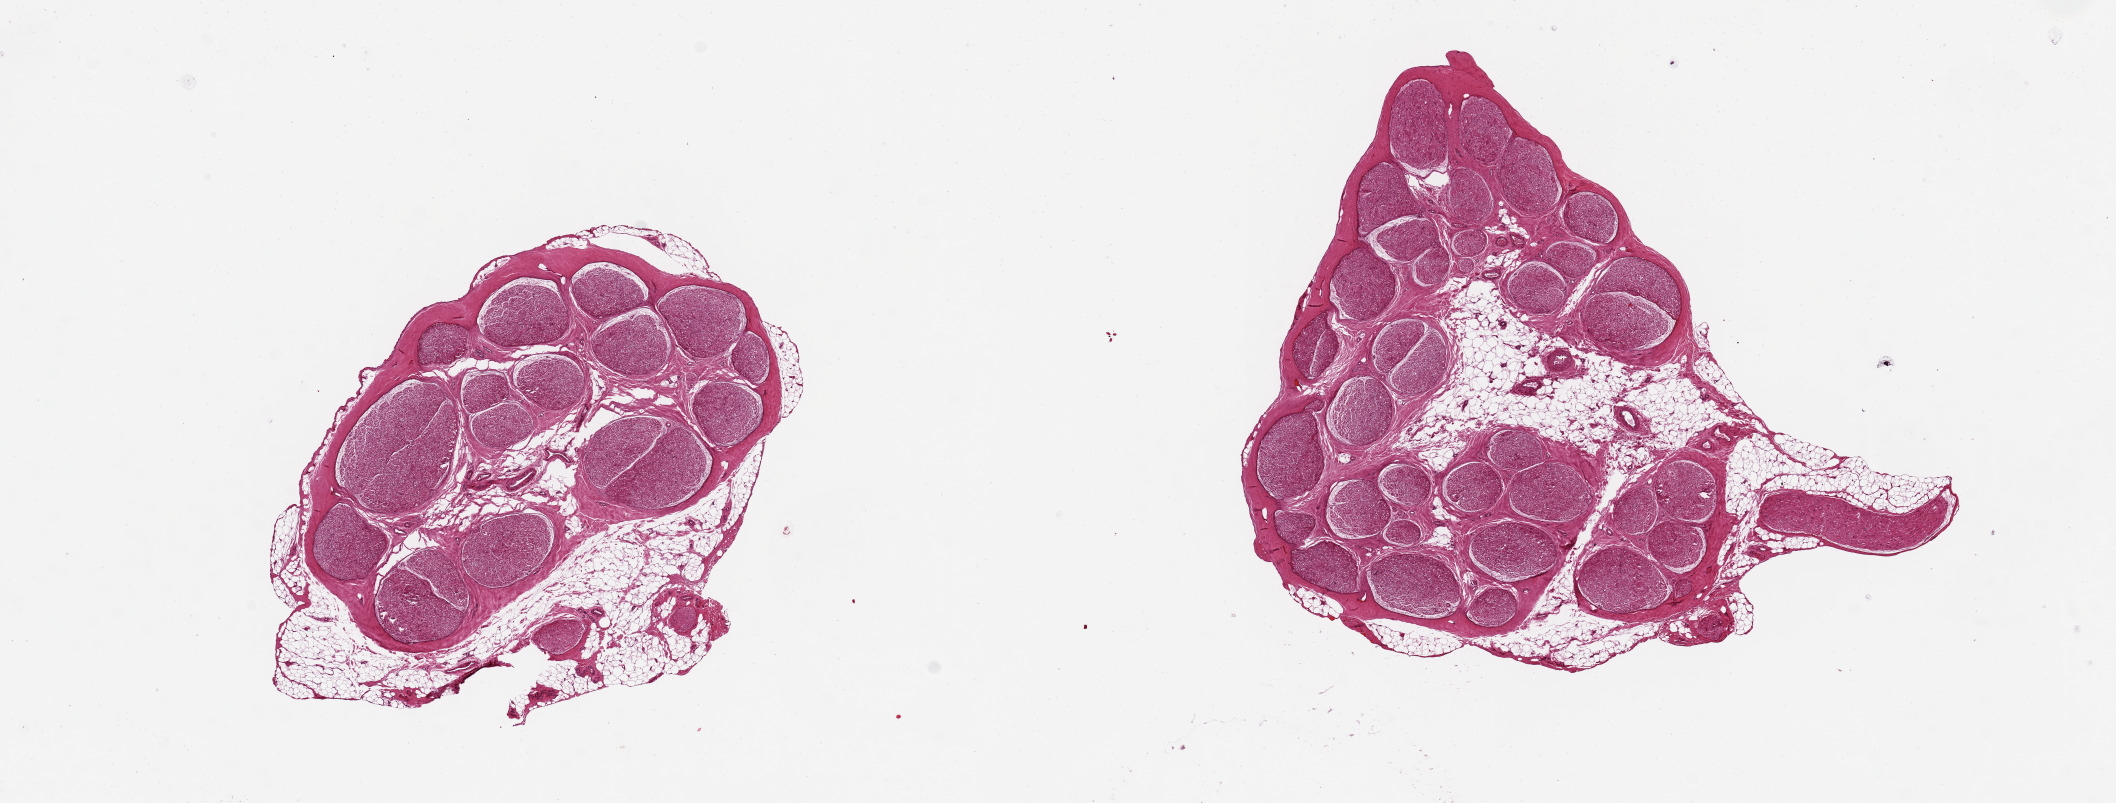
Digitized haematoxylin and eosin-stained section — low-resolution overview of the scanned area, about 16.7 x 6.4 mm. PAXgene-fixed paraffin-embedded (PFPE) section. Sampled site (target tissue): tibial nerve. Tissue donor sample. Male donor.
• reviewer comment on this tissue sample: 2 pieces, 5x4 & 5x3 mm; ~20% adipose in and around nerve